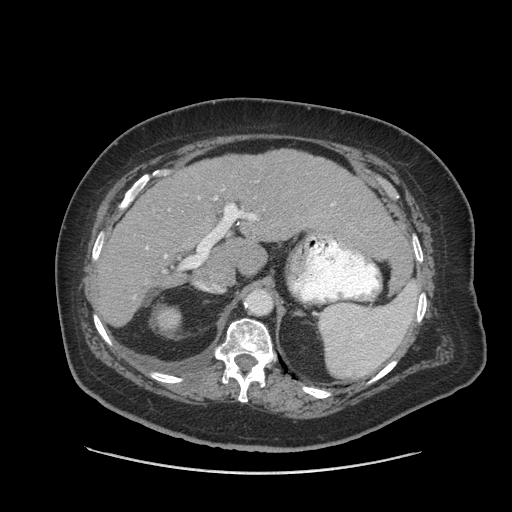
Contrast-enhanced abdominal CT (liver protocol), one axial slice; slice 53 of 91 in the series (ordered by position); soft-tissue window (W 400 / L 40 HU); 2.5 mm slice thickness; 512 × 512 image matrix, field of view 420 × 420 mm. From the clinical record (not read from this slice): diagnosis: hepatocellular carcinoma (patient treated with transarterial chemoembolisation; whether this scan precedes or follows treatment is not stated here); TNM stage (as recorded): Stage-I; Child-Pugh class: A; tumour differentiation: well differentiated; tumour nodularity: uninodular.
Structures marked on this image (semi-automatically segmented with operator editing):
- liver parenchyma outside the tumour (the mass and vessels are separate outlines, so this box may not span the whole liver): box from (x=95, y=150) to (x=398, y=326) px
- liver vessels: (x=146, y=204)–(x=334, y=258)